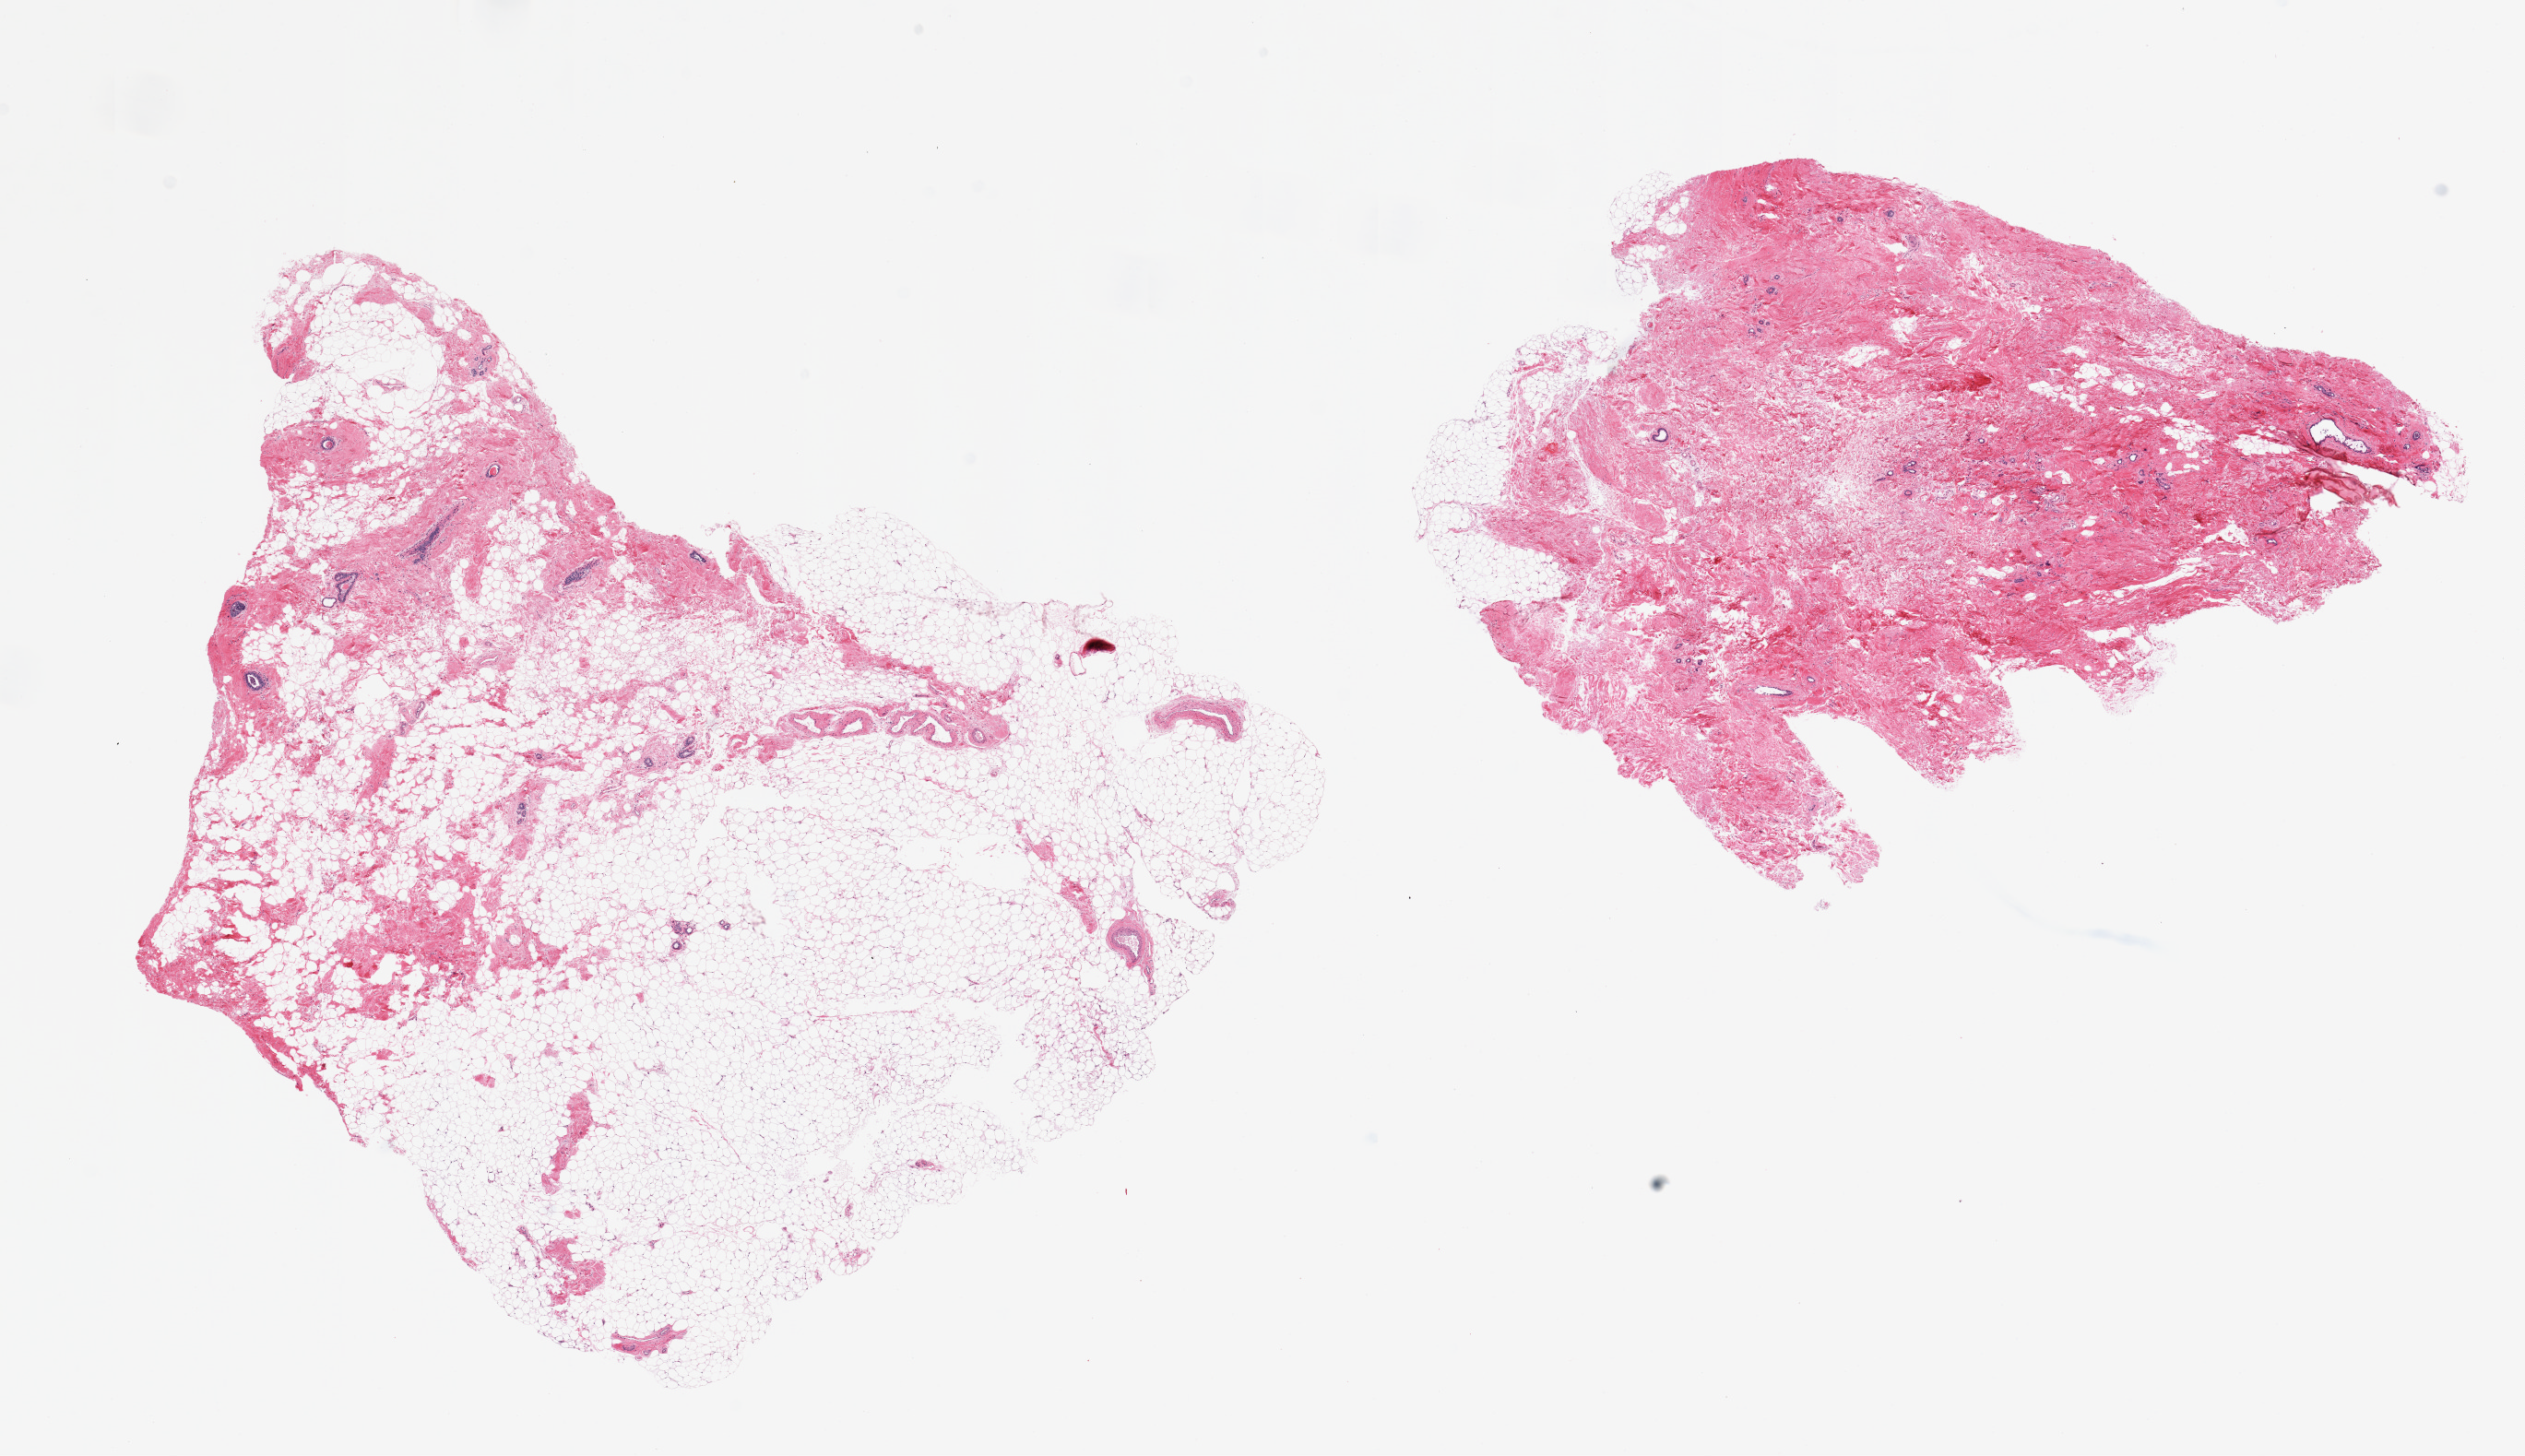
Whole-slide image, haematoxylin and eosin stain, brightfield, shown as a low-resolution overview of the whole scanned area (about 21.7 x 12.5 mm), PAXgene-fixed, paraffin-embedded tissue, section of breast (target tissue), tissue donor sample. Donor: female.
Review note (as recorded): 2 pieces; atrophic; ducts without lobular units; 70 & 10% fat.